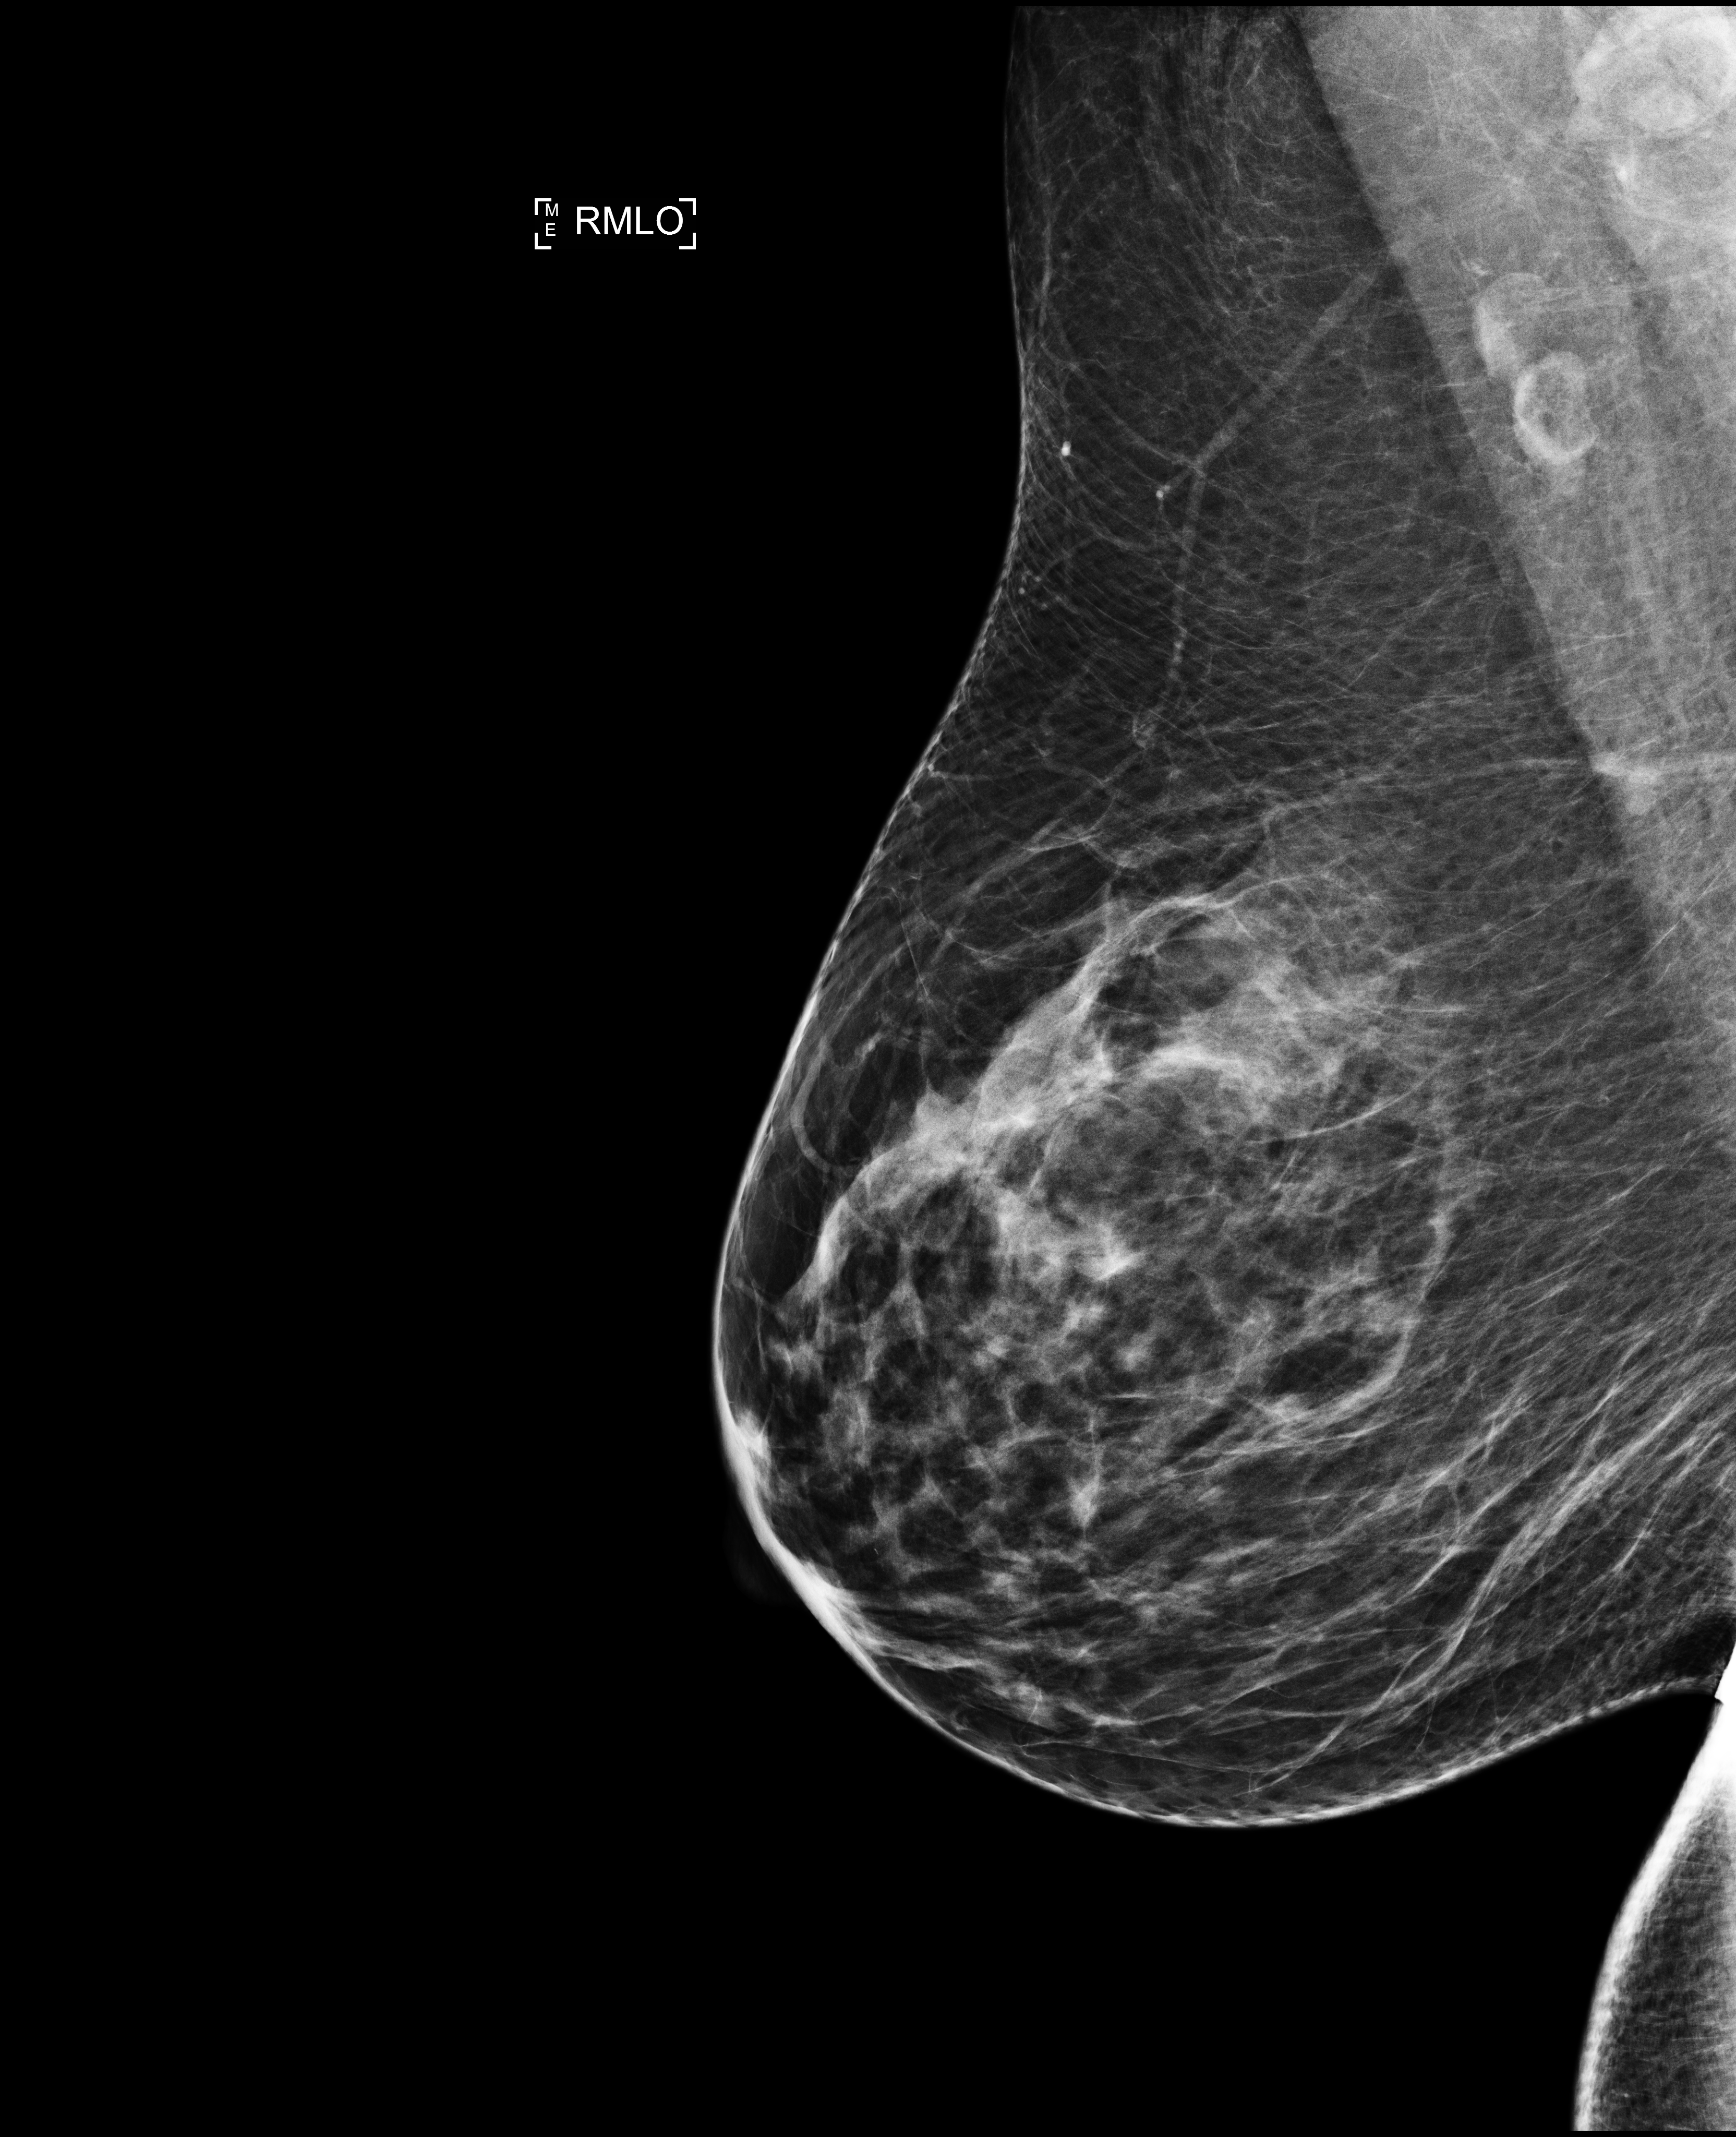
Annual screening mammography examination, compressed breast thickness 69 mm. Female patient, age 52 years.
Image type: full-field digital mammogram. Breast: right. Projection: mediolateral oblique (MLO) view.